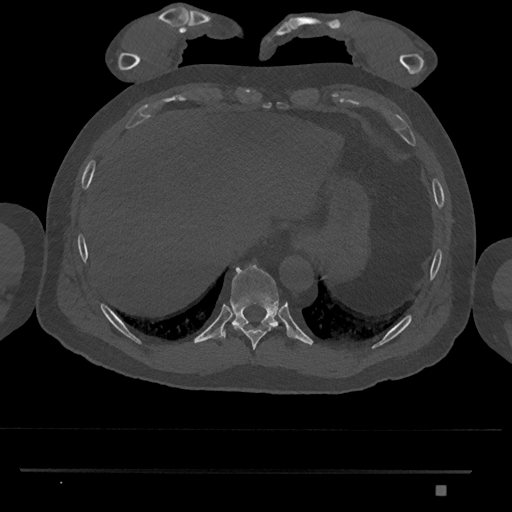
CT including the spine, one axial slice; reconstruction kernel Br40s/3; bone window (W 1800 / L 400 HU); 0.5 mm slice thickness; 512 × 512 image matrix, field of view 429 × 429 mm. Male patient, age 65 years. Case-level facts recorded for this patient, not image findings: primary cancer: prostate.
Structures marked on this image (semi-automatically segmented with operator editing):
- T10 vertebra: bounding box (x1, y1, x2, y2) in pixels: (221, 264, 279, 340)
- T9 vertebra: (232, 324, 278, 350)